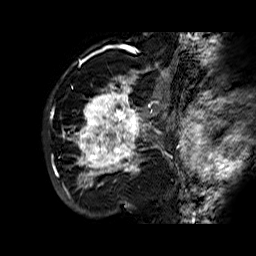
Breast MRI (dynamic contrast-enhanced), one sagittal slice; position 45 of 60 along the scan axis; dynamic contrast-enhanced series, time point 2 of 6 at this slice position (early post-contrast); 1.5 T; TE 6.3 ms, TR 32.4 ms; 256 × 256 image matrix, field of view 200 × 200 mm. Female patient. Case-level facts recorded for this patient, not image findings: setting: breast cancer imaged before/during neoadjuvant chemotherapy; receptor status: HR-positive, HER2-negative.
Outlined on this slice (semi-automatically segmented with operator editing):
- analysis volume of interest (the breast-tissue region the enhancement analysis was run in; not a lesion): bounding box (x1, y1, x2, y2) in pixels: (68, 72, 177, 183)
- tumour enhancement mask (voxels above the 100 % enhancement threshold inside the analysis volume of interest): (69, 72, 167, 183)